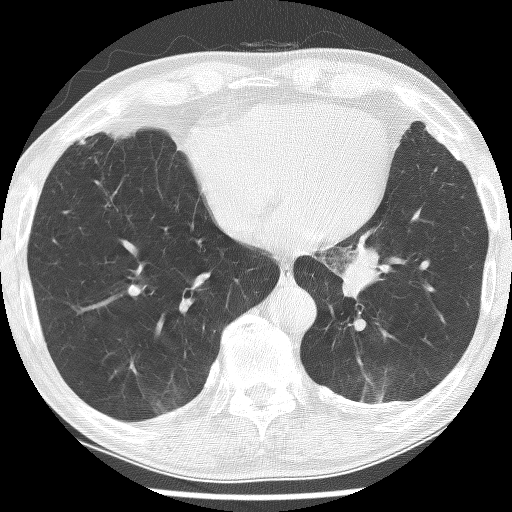
Low-dose screening chest CT, one axial slice; position 58 of 226 along the scan axis; reconstruction kernel BONE; 120 kVp; lung window (W 1500 / L -600 HU); 2.5 mm slice thickness; 512 × 512 image matrix.
Outlined on this slice (outlined manually by an expert reader):
- lesion 1 (tumor, lower lobe of left lung): bounding box <341,248,380,298> (left, top, right, bottom; pixels)